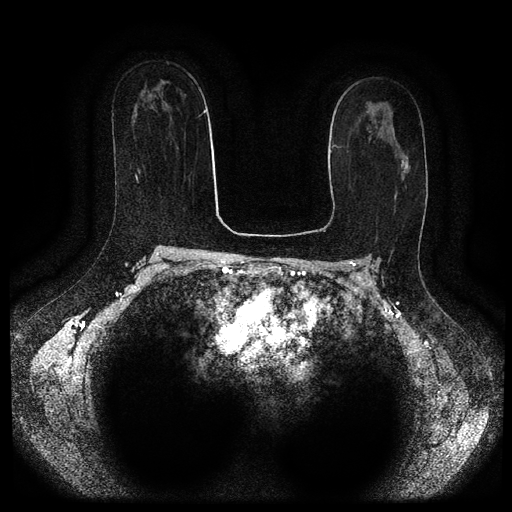
Breast MRI (dynamic contrast-enhanced, multi-phase), one axial slice; position 63 of 116 along the scan axis; dynamic contrast-enhanced series, time point 2 of 5 at this slice position (early post-contrast); 1.5 T; TE 2.7 ms, TR 5.4 ms; 2 mm slice thickness; 512 × 512 image matrix, field of view 340 × 340 mm. Female patient, age 47 years.
Annotated regions visible in this slice (semi-automatically segmented with operator editing):
- breast lesion (labelled benign in the annotation): box from (x=393, y=130) to (x=395, y=139) px